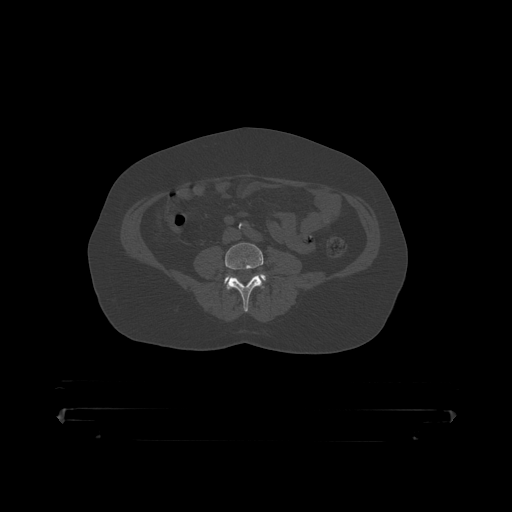
CT including the spine, one axial slice. Position 60 of 390 along the scan axis. Reconstruction kernel STANDARD. 120 kVp. Bone window (W 1800 / L 400 HU). 1.25 mm slice thickness. 512 × 512 image matrix, field of view 650 × 650 mm. Patient: male, 60 years. Case-level facts recorded for this patient, not image findings: primary cancer: prostate.
Structures marked on this image (semi-automatically segmented with operator editing):
- L4 vertebra: bounding box <226,243,267,313> (left, top, right, bottom; pixels)
- L5 vertebra: <225,274,267,282>